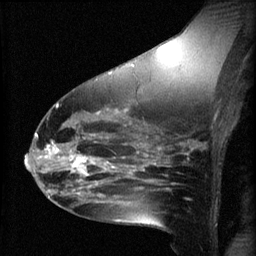
Breast MRI (dynamic contrast-enhanced), one sagittal slice. Position 33 of 60 along the scan axis. 3 images stored at this slice position (order not interpretable as contrast timing). 1.5 T. TE 4.2 ms, TR 8.2 ms. 256 × 256 image matrix, field of view 180 × 180 mm. Female patient, age 49 years.
Annotated regions visible in this slice (semi-automatically segmented with operator editing):
- analysis volume of interest (the breast-tissue region the enhancement analysis was run in; not a lesion): bounding box <45,136,109,187> (left, top, right, bottom; pixels)
- tumour enhancement mask (voxels above the 70 % enhancement threshold inside the analysis volume of interest): <45,138,109,187>